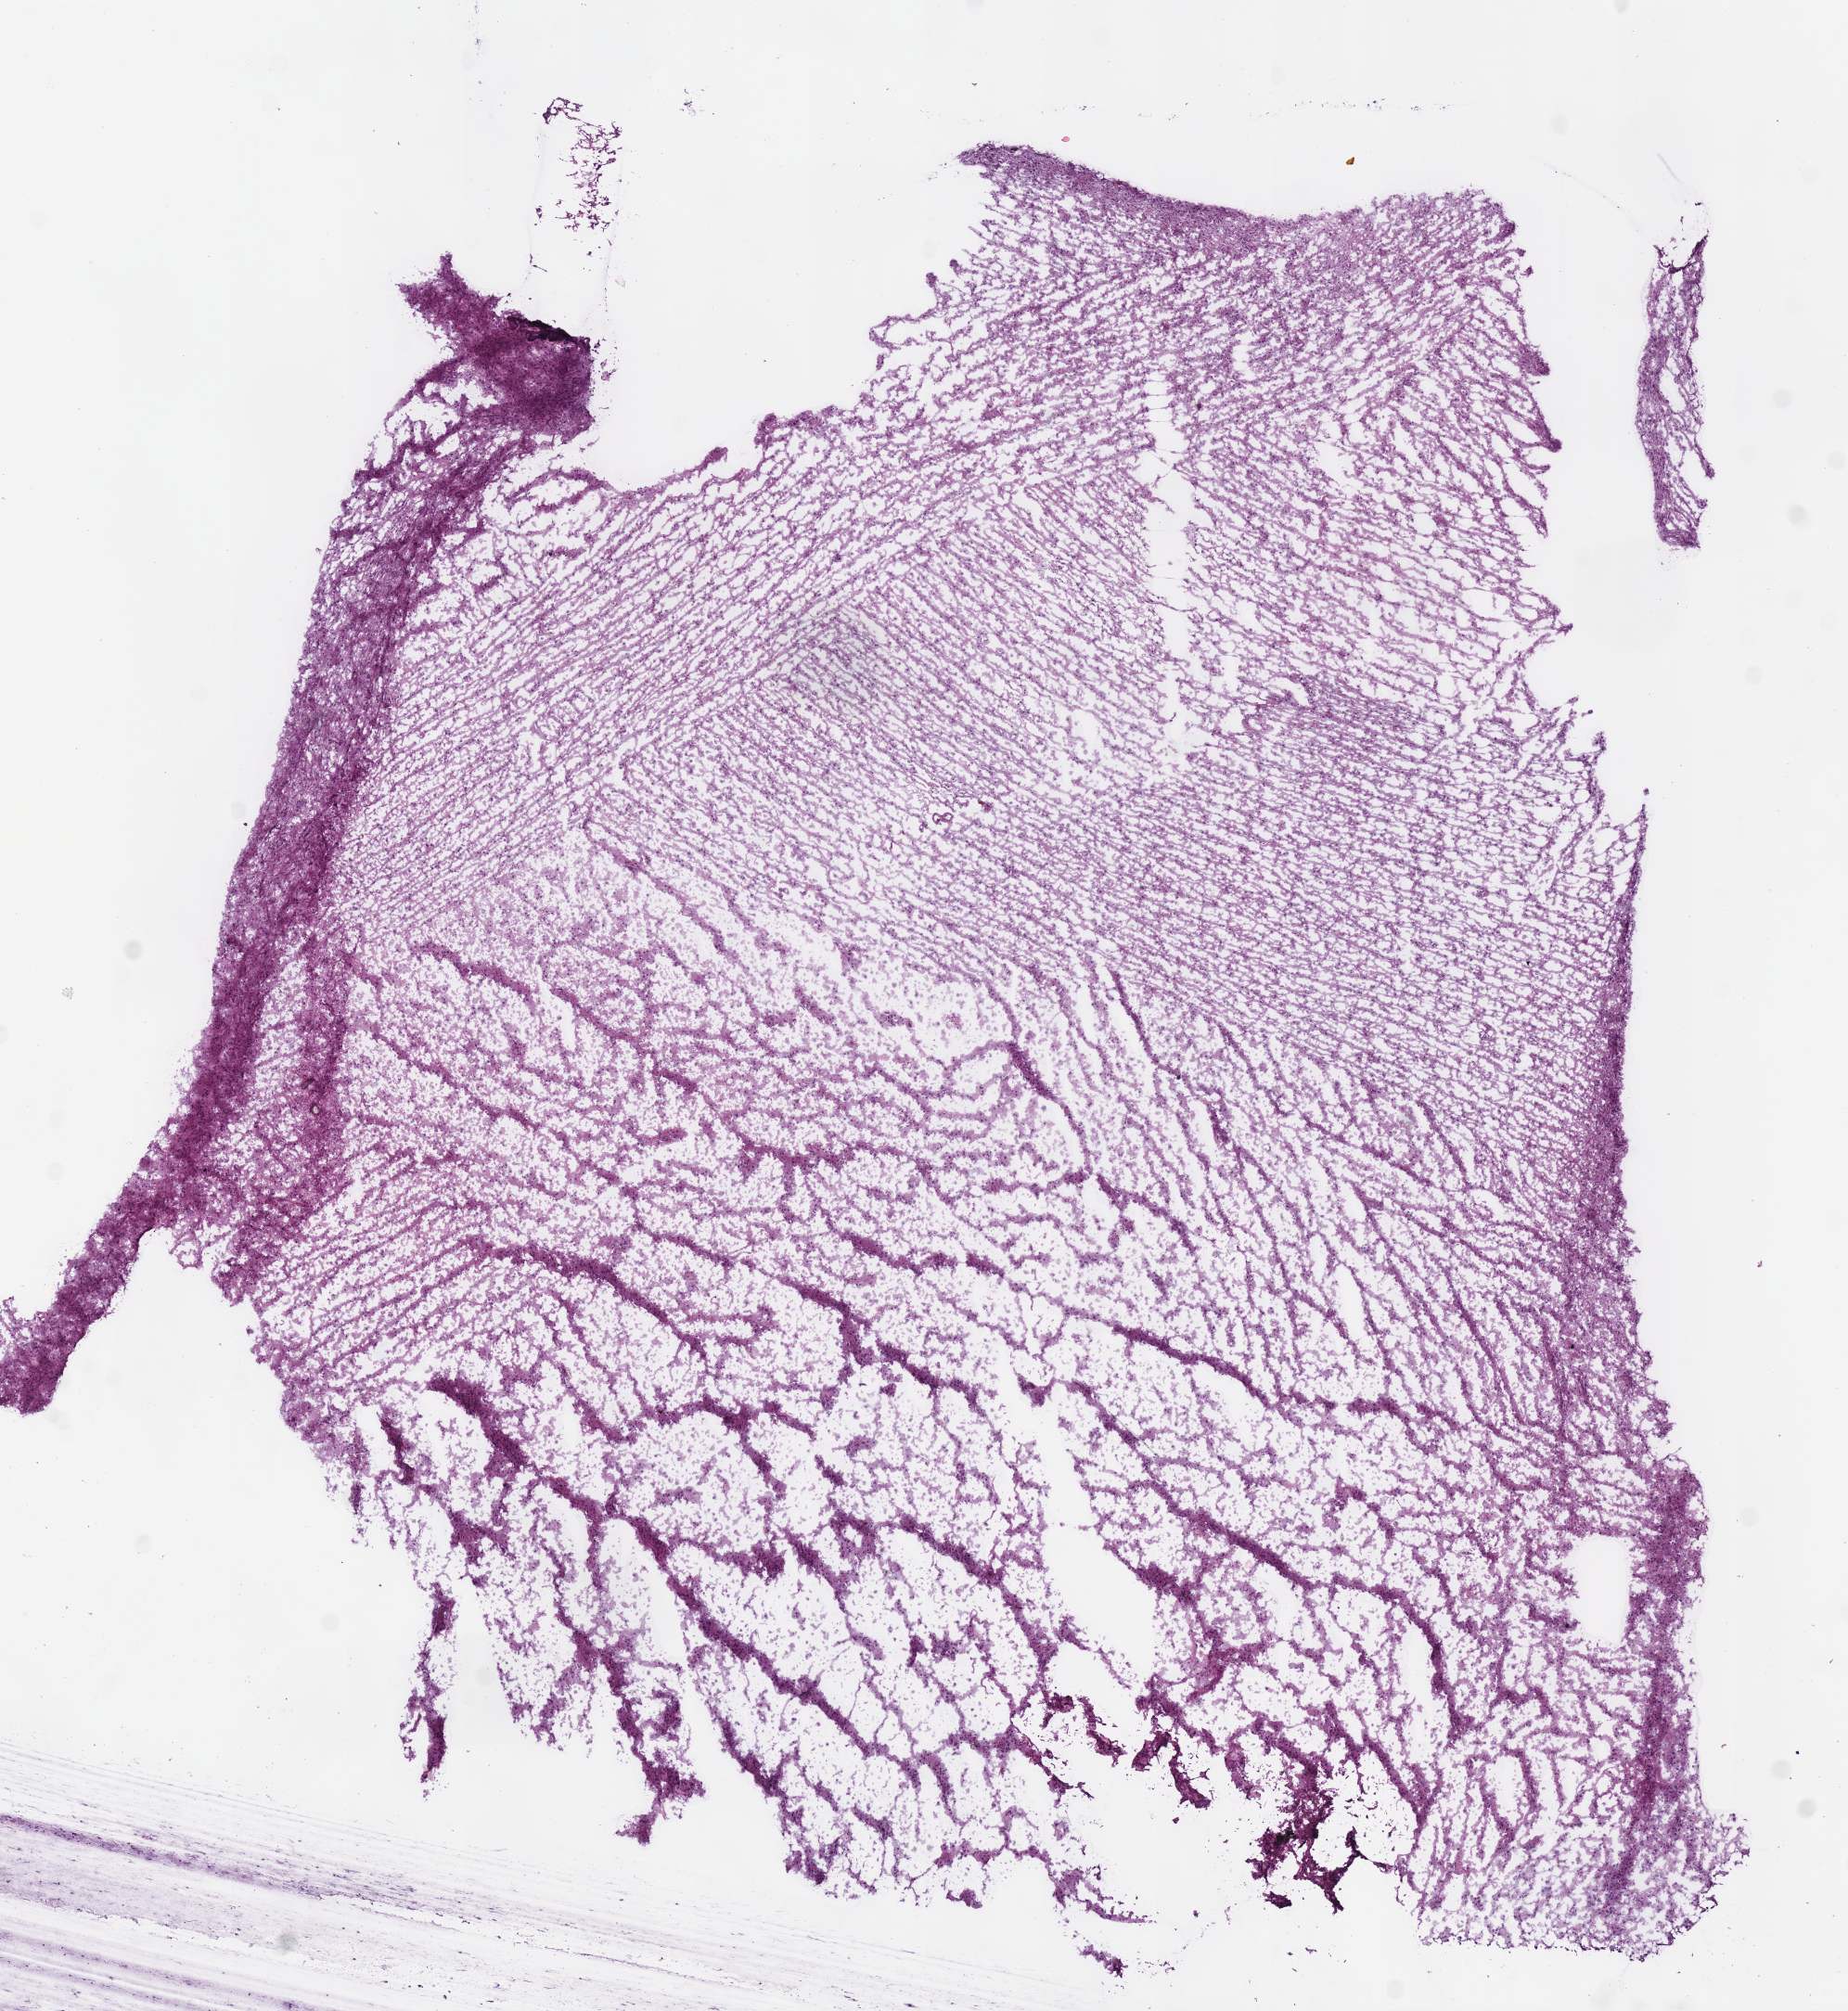
H&E-stained whole-slide image, a low-resolution overview of the entire scanned area, about 7.8 x 8.5 mm (acquisition: 40x scan). Frozen section. Sample: primary tumour, brain. Male patient; age at initial diagnosis 35 years. Histologic grade: G2 (moderately differentiated). Slide review estimates, as recorded: tumour cells 100%, tumour nuclei 75%, normal cells 0%, stromal cells 0%, necrosis 0%.
Laterality: left. Diagnosis: Oligodendroglioma, NOS.